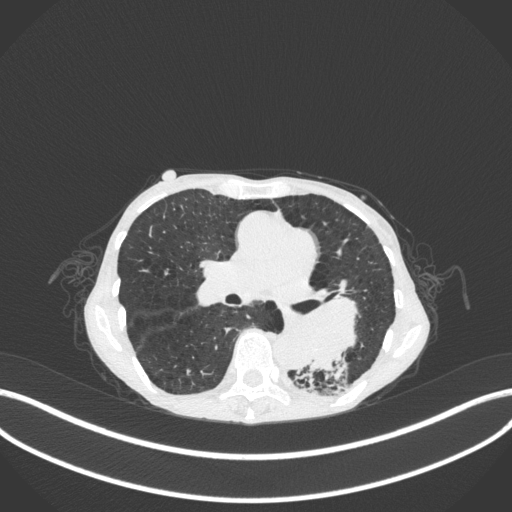
Chest CT, one axial slice. Slice 150 of 347 in the series (ordered by position). 120 kVp. Lung window (W 1500 / L -600 HU). 1 mm slice thickness. 512 × 512 image matrix, field of view 400 × 400 mm. Patient: female, 70 years. Case-level facts recorded for this patient, not image findings: clinical TNM (as recorded): T3 N0 M0; histopathological grade: G3.
Structures marked on this image (bounding box drawn by a radiologist):
- lung tumour (recorded histology: small cell carcinoma): bounding box (x1, y1, x2, y2) in pixels: (272, 290, 365, 374)